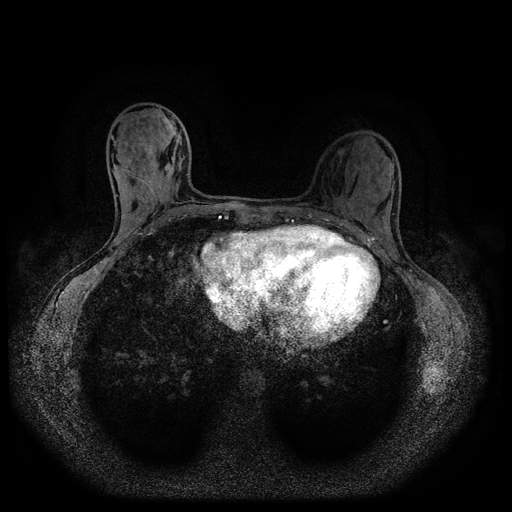
Breast MRI (dynamic contrast-enhanced, multi-phase), one axial slice. Slice 41 of 116 in the series (ordered by position). Dynamic contrast-enhanced series, time point 2 of 5 at this slice position (early post-contrast). 1.5 T. TE 2.7 ms, TR 5.4 ms. 512 × 512 image matrix. Female patient, age 32 years.
Outlined on this slice (semi-automatic segmentation, software-assisted and operator-edited):
- breast lesion (labelled benign in the annotation): bounding box [x1, y1, x2, y2] px = [162, 161, 174, 176]